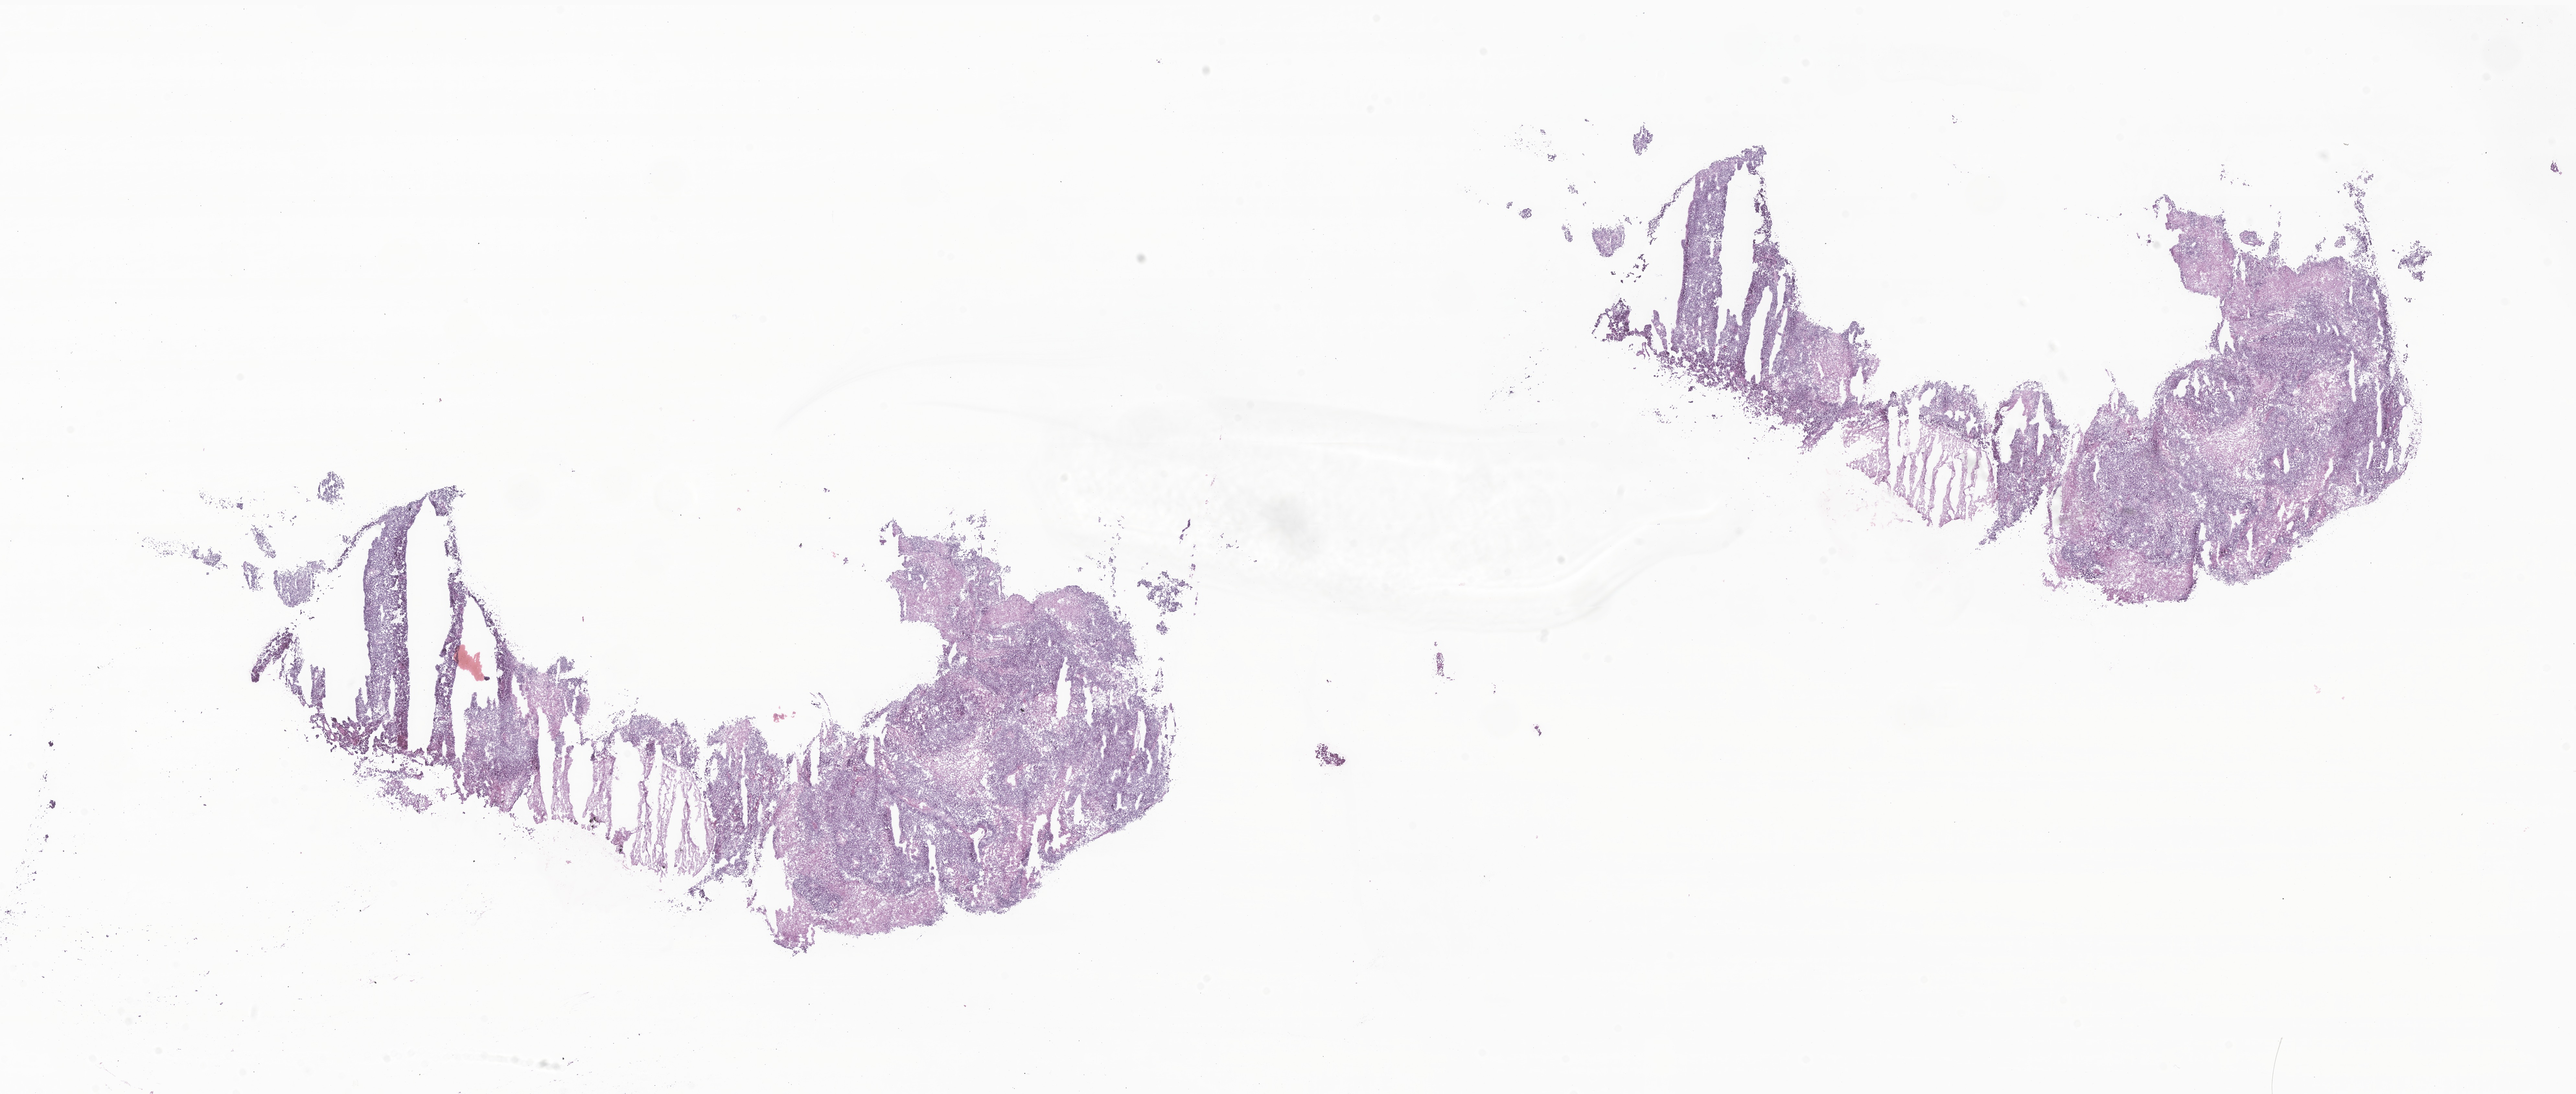
Hematoxylin and eosin (H&E) whole-slide image of tumor tissue from the brain, a low-resolution overview of the entire scanned area, about 33.5 x 14.2 mm. Cryosection (OCT / tissue freezing medium). Male patient, age 117 months.
Recorded diagnosis: Medulloblastoma, NOS.